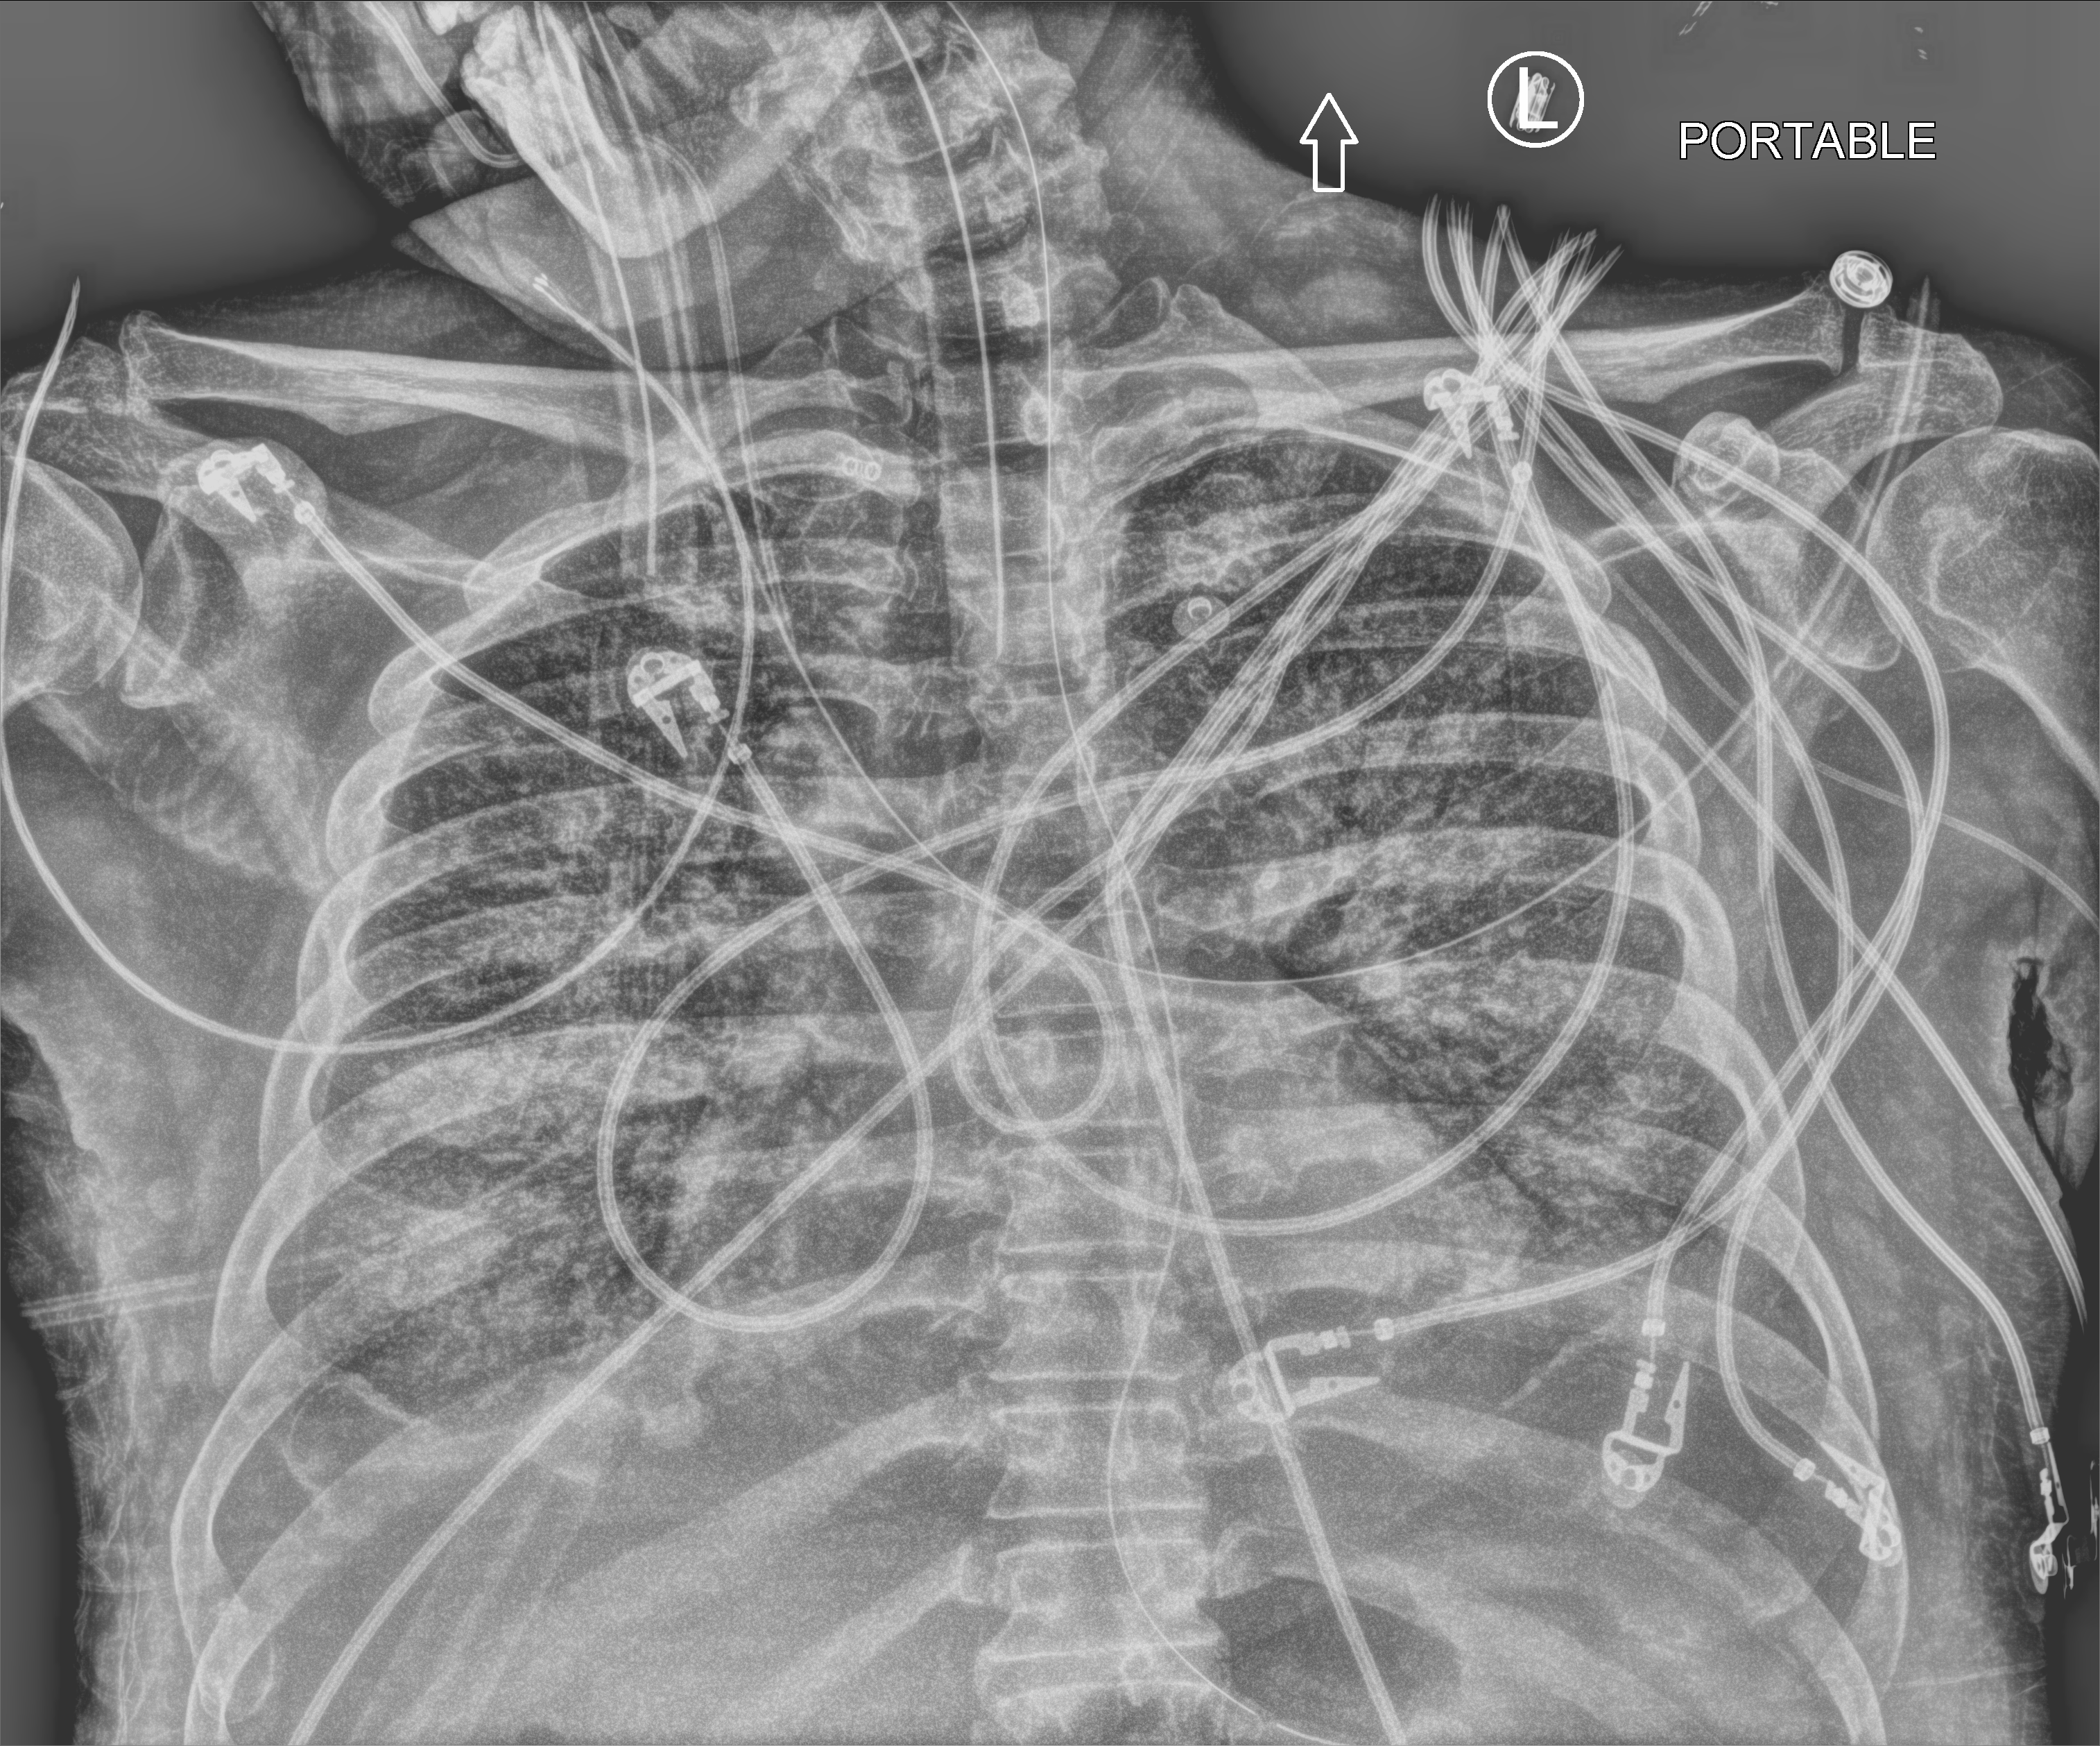
Portable chest radiograph, anteroposterior (AP) projection. Male patient hospitalised with COVID-19, age 60–74 years.
Admission-level facts for this patient (not findings on this image; timing relative to this image not recorded):
- other chronic lung disease (admission record): no
- smoking status (admission record): never
- diabetes (admission record): no